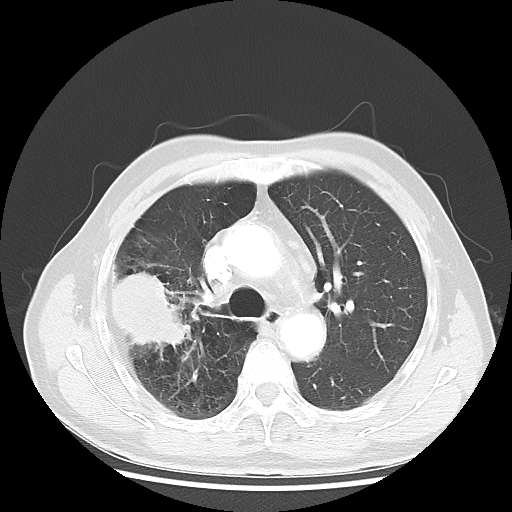
Chest CT, one axial slice. Position 33 of 50 along the scan axis. Reconstruction kernel LUNG. Lung window (W 1500 / L -600 HU). 5 mm slice thickness. 512 × 512 image matrix, field of view 360 × 360 mm. Patient: male, 69 years. Case-level facts recorded for this patient, not image findings: clinical TNM (as recorded): T3 N0 M0.
Structures marked on this image (rectangle marked by the reading radiologist):
- lung tumour (recorded histology: adenocarcinoma): bounding box (x1, y1, x2, y2) in pixels: (109, 265, 195, 351)